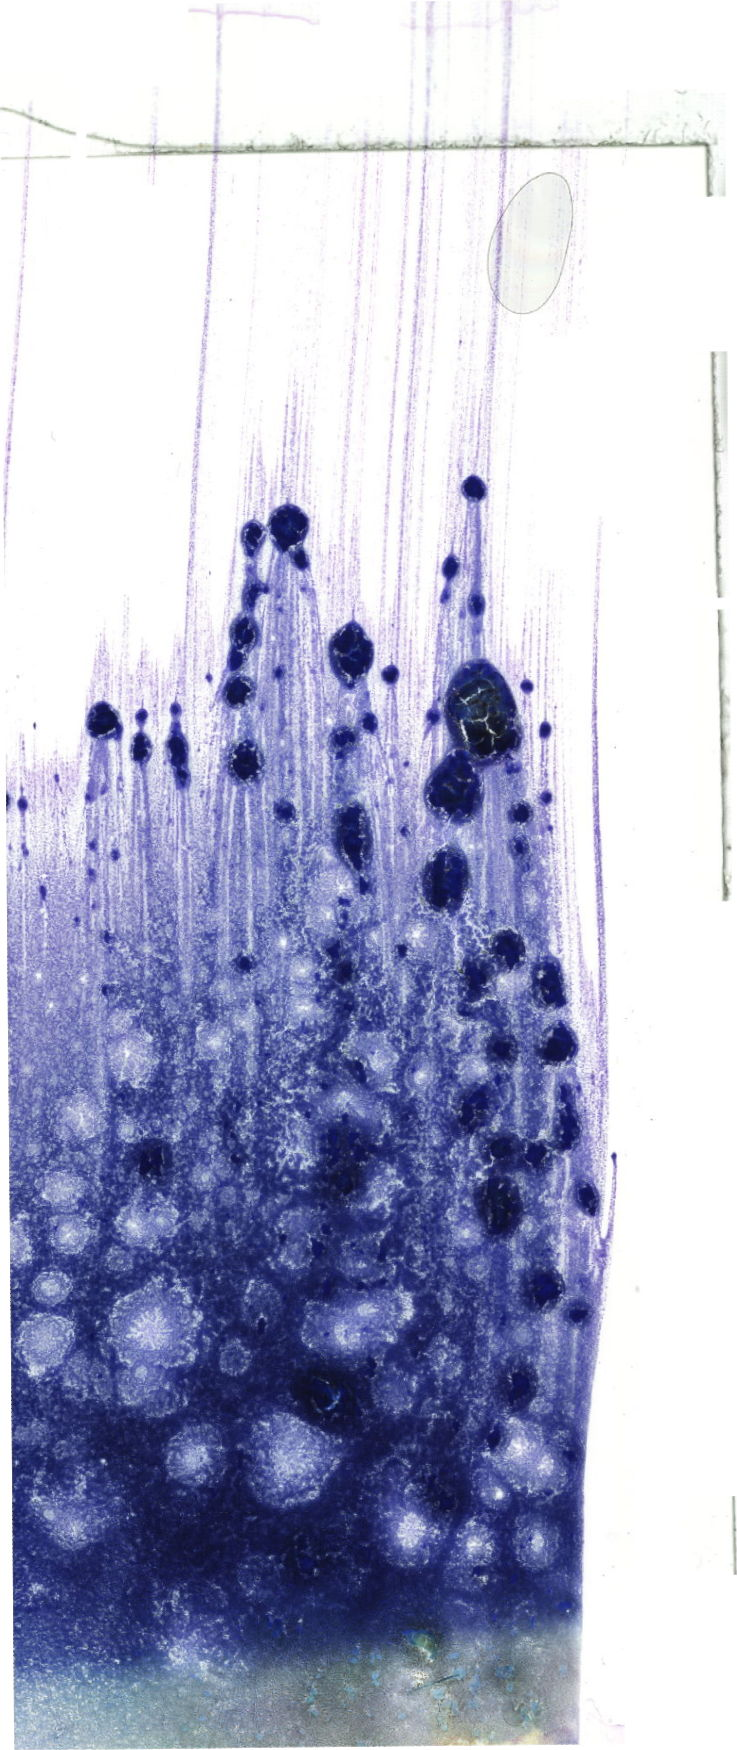
Bone marrow aspirate smear, May-Grünwald-Giemsa (MGG) stain, whole-slide image, a low-resolution overview of the entire scanned area, about 20.9 x 49.6 mm. Male patient.
Diagnosis: Acute Myeloid Leukemia with Maturation.